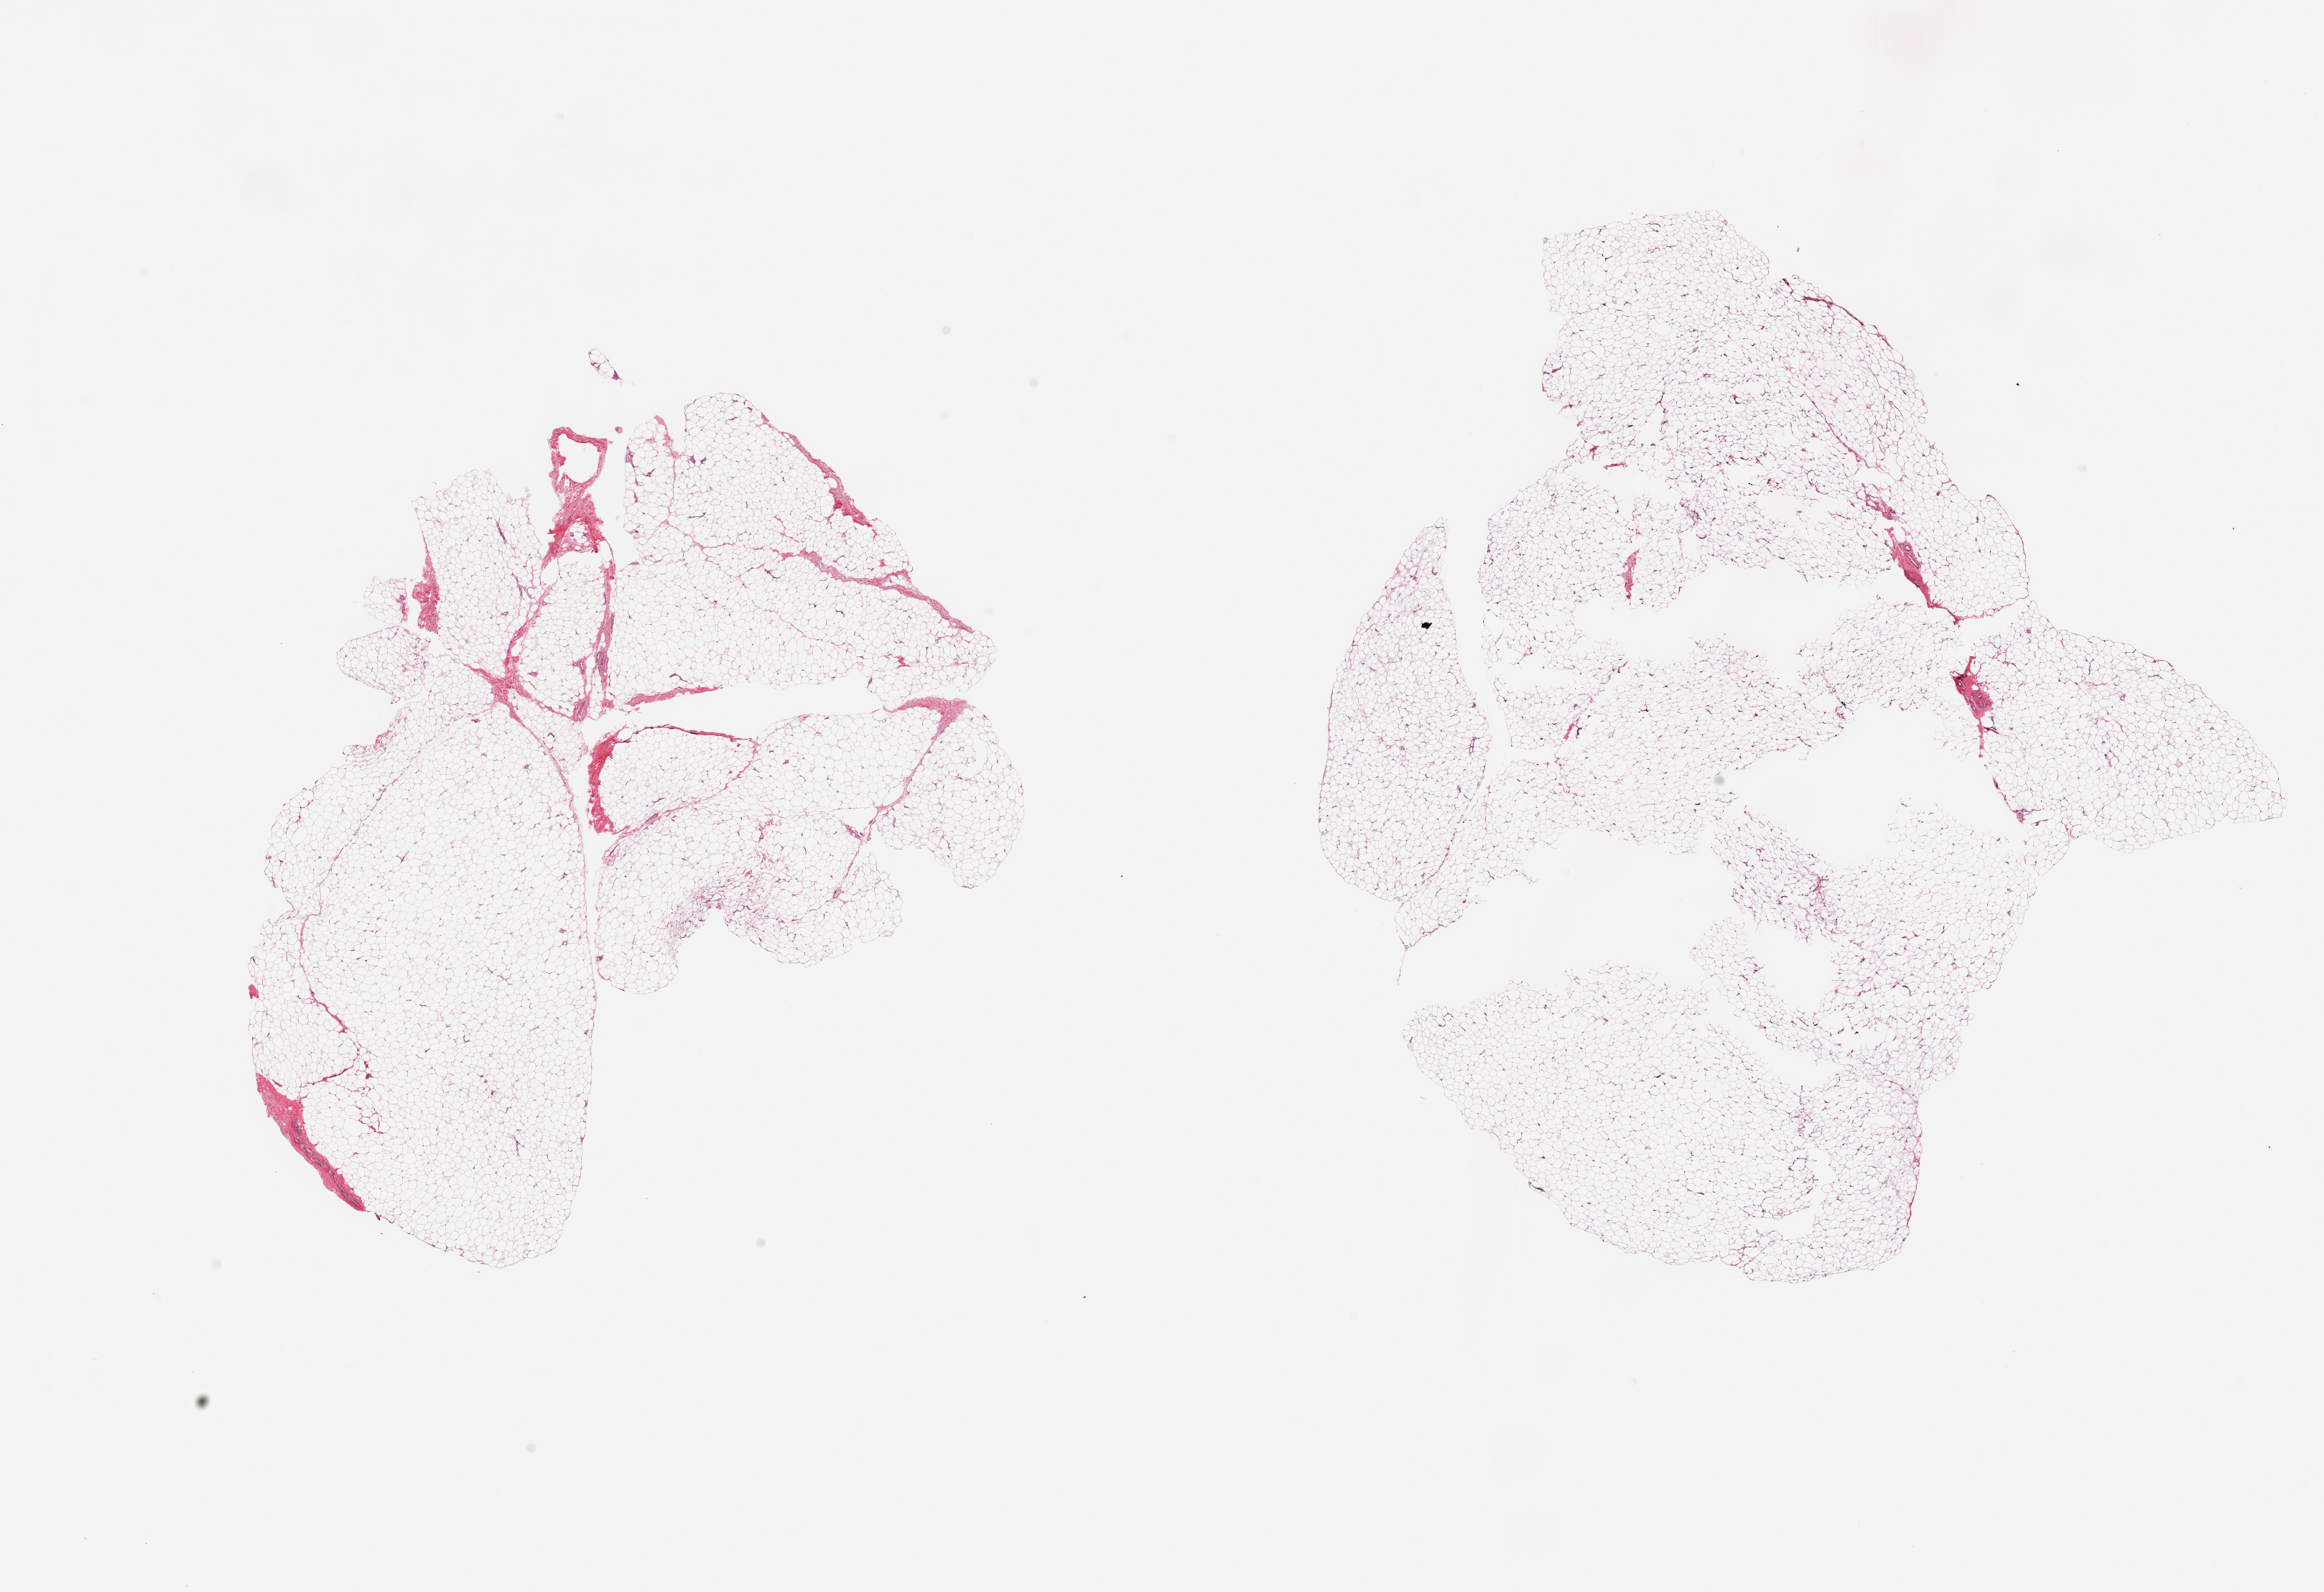
Hematoxylin and eosin (H&E) whole-slide image — shown as a low-resolution overview of the whole scanned area (about 25.6 x 17.5 mm), PAXgene-fixed, paraffin-embedded tissue, target tissue: adipose tissue, tissue donor sample.
Pathologist's review note for this sample: 2 pieces, ~5% fascia/vascular elements.